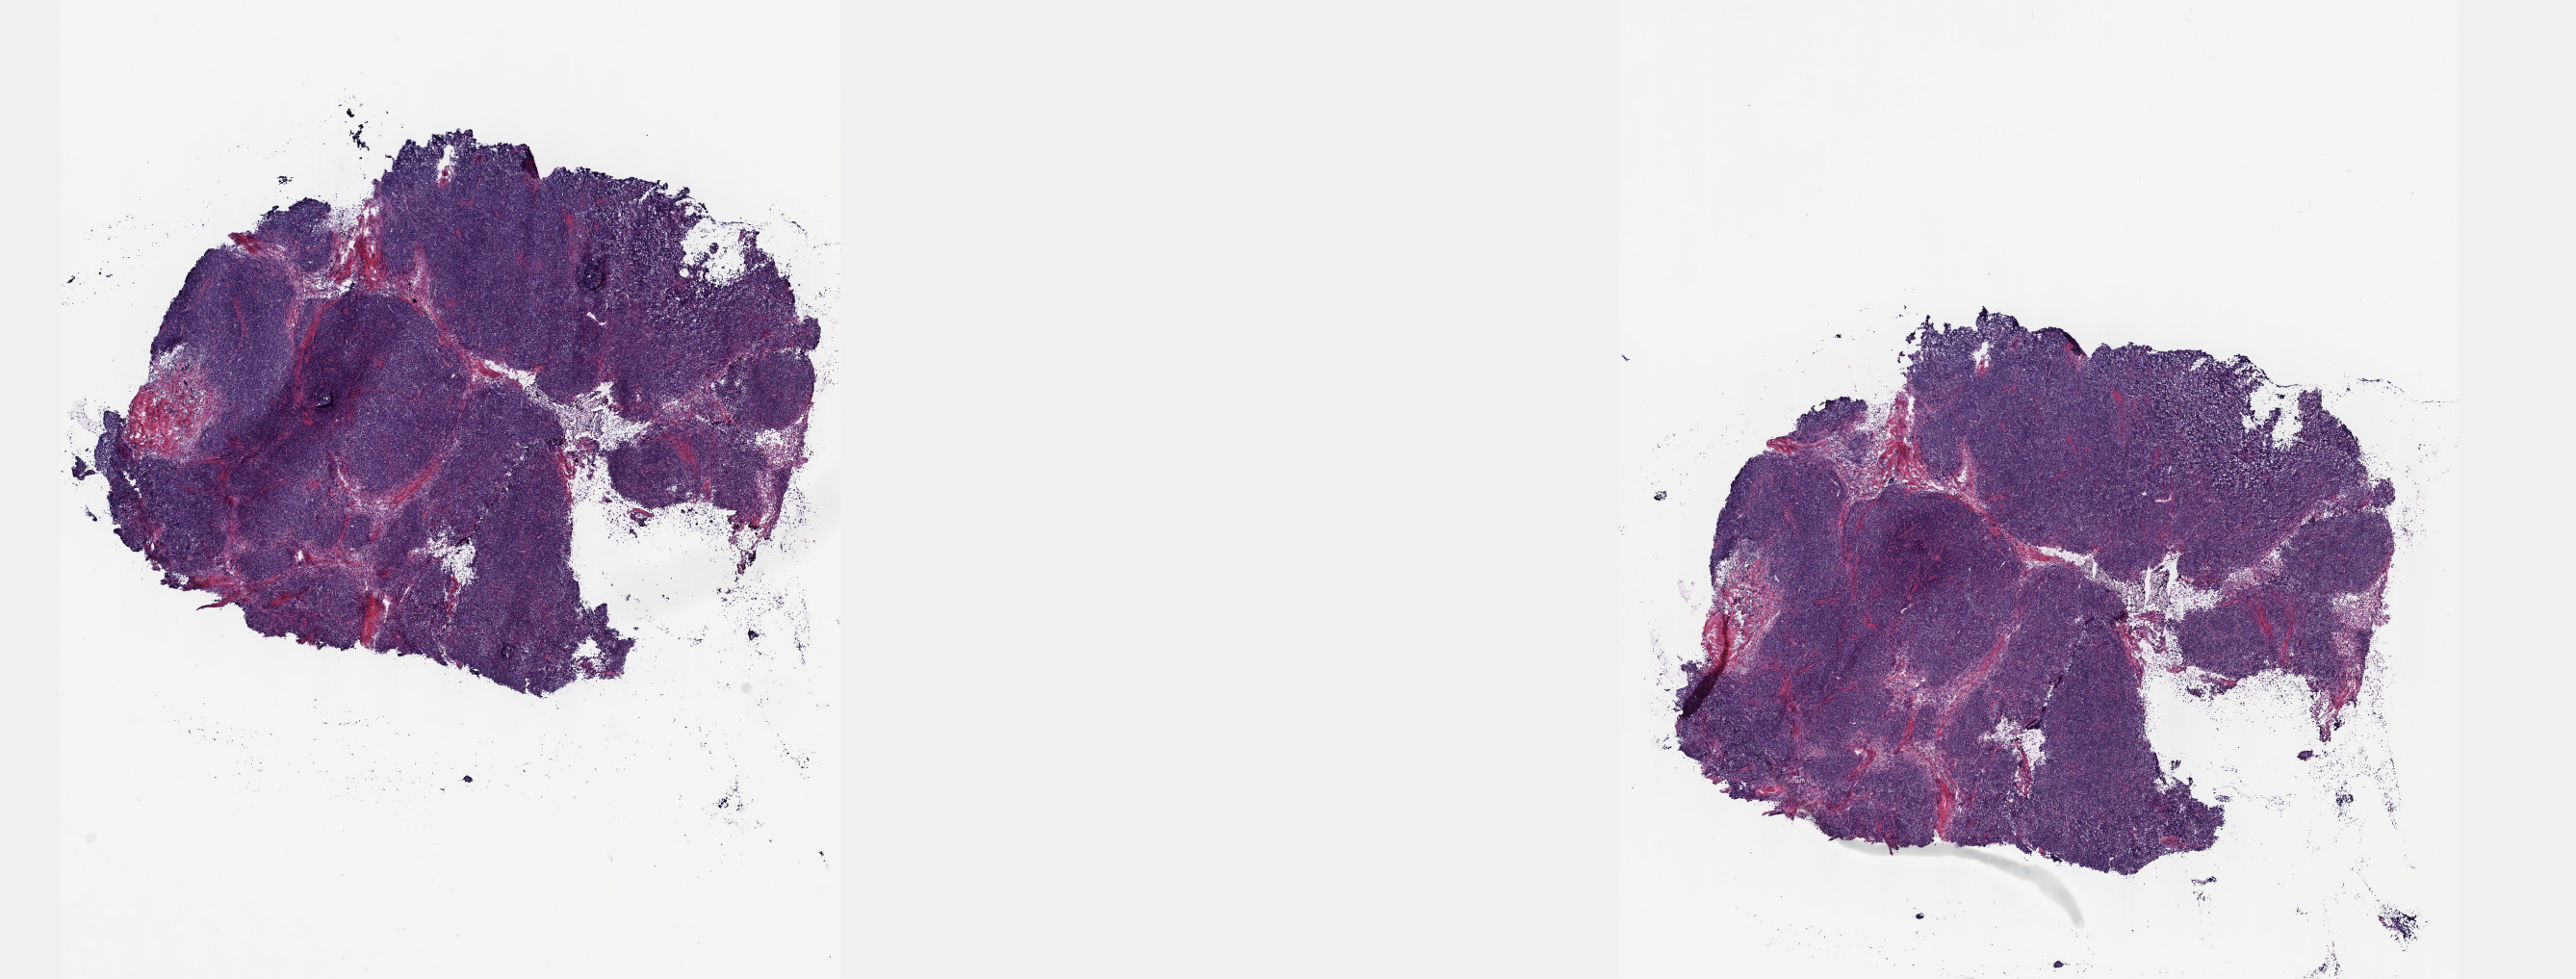
H&E whole-slide image — low-resolution overview of the scanned area, about 21.6 x 8.2 mm (from a 40x scan); frozen section from the top of the tissue portion; thymus, primary tumour sample. Male, age 68 years at initial diagnosis. Pathologist review of this section (percent, as recorded): tumour cells 100%, tumour nuclei 98%.
Histologic diagnosis: Thymoma, type AB, NOS (anterior mediastinum).